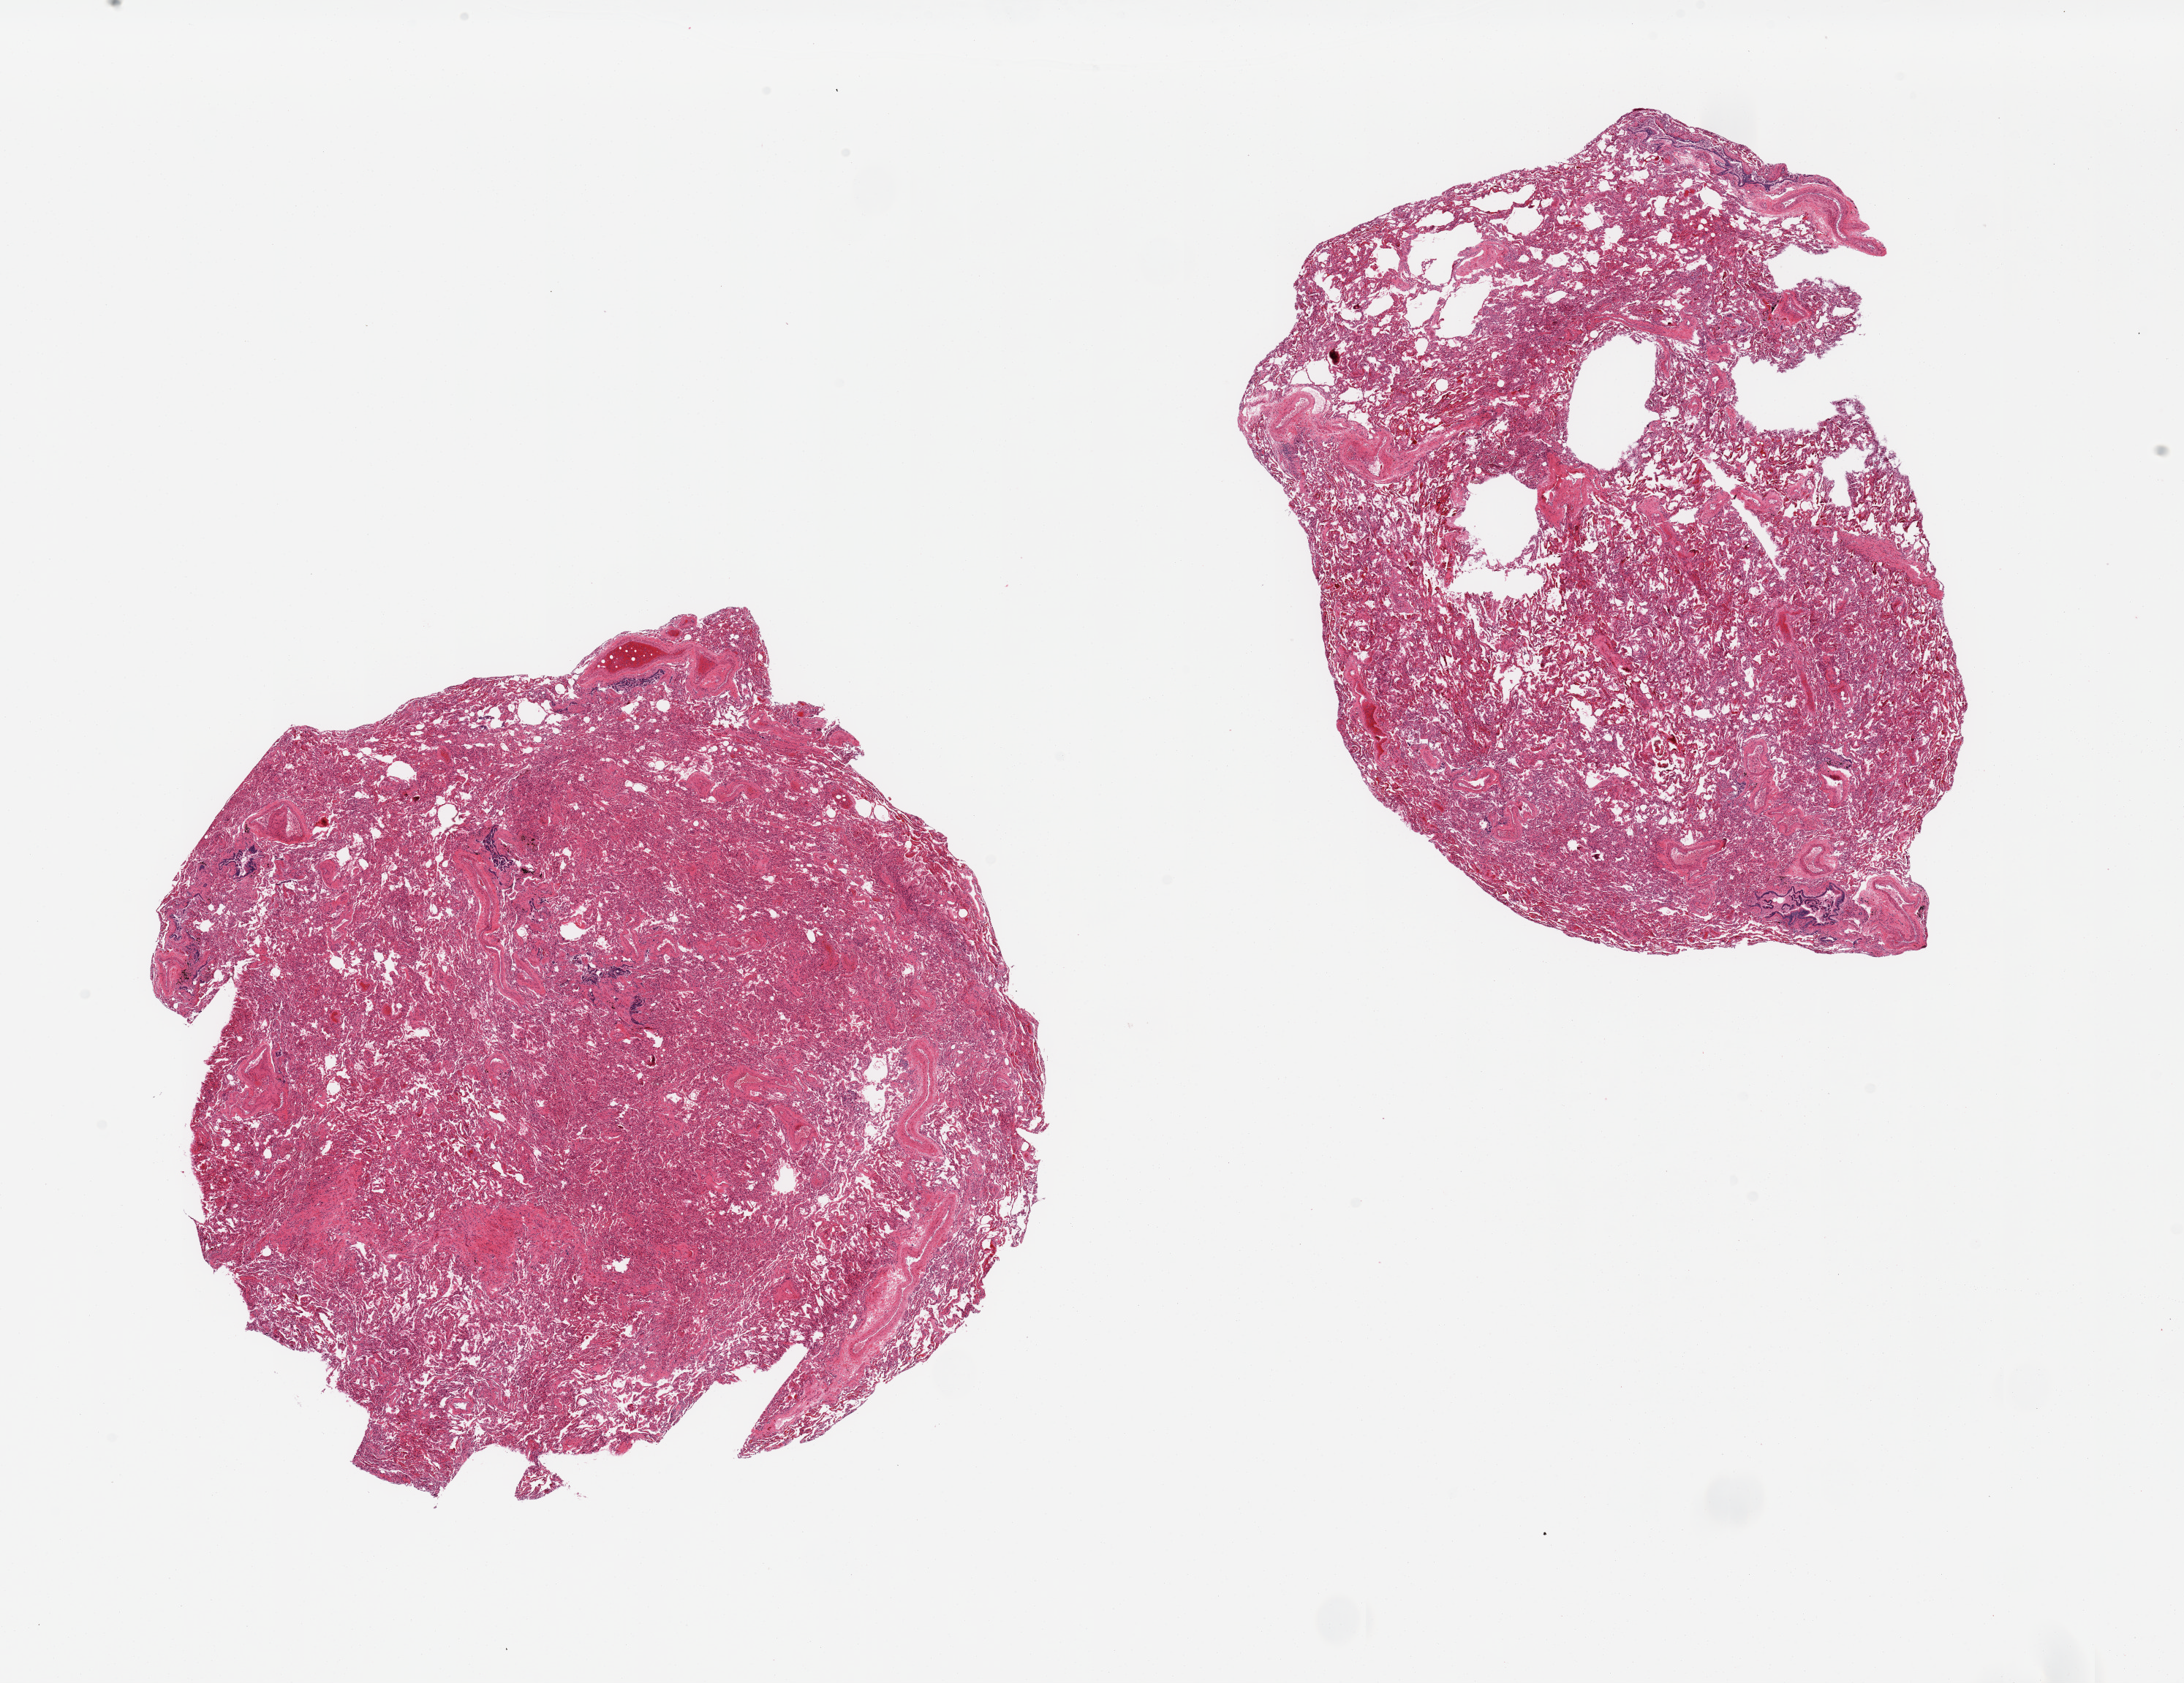
H&E whole-slide image — shown as a low-resolution overview of the whole scanned area (about 23.6 x 18.2 mm, acquisition: 20x scan), PAXgene-fixed paraffin-embedded (PFPE) section, target tissue: lung, tissue donor sample. Male donor.
* review note (as recorded): 2 pieces; atelectasis with patchy emphysema